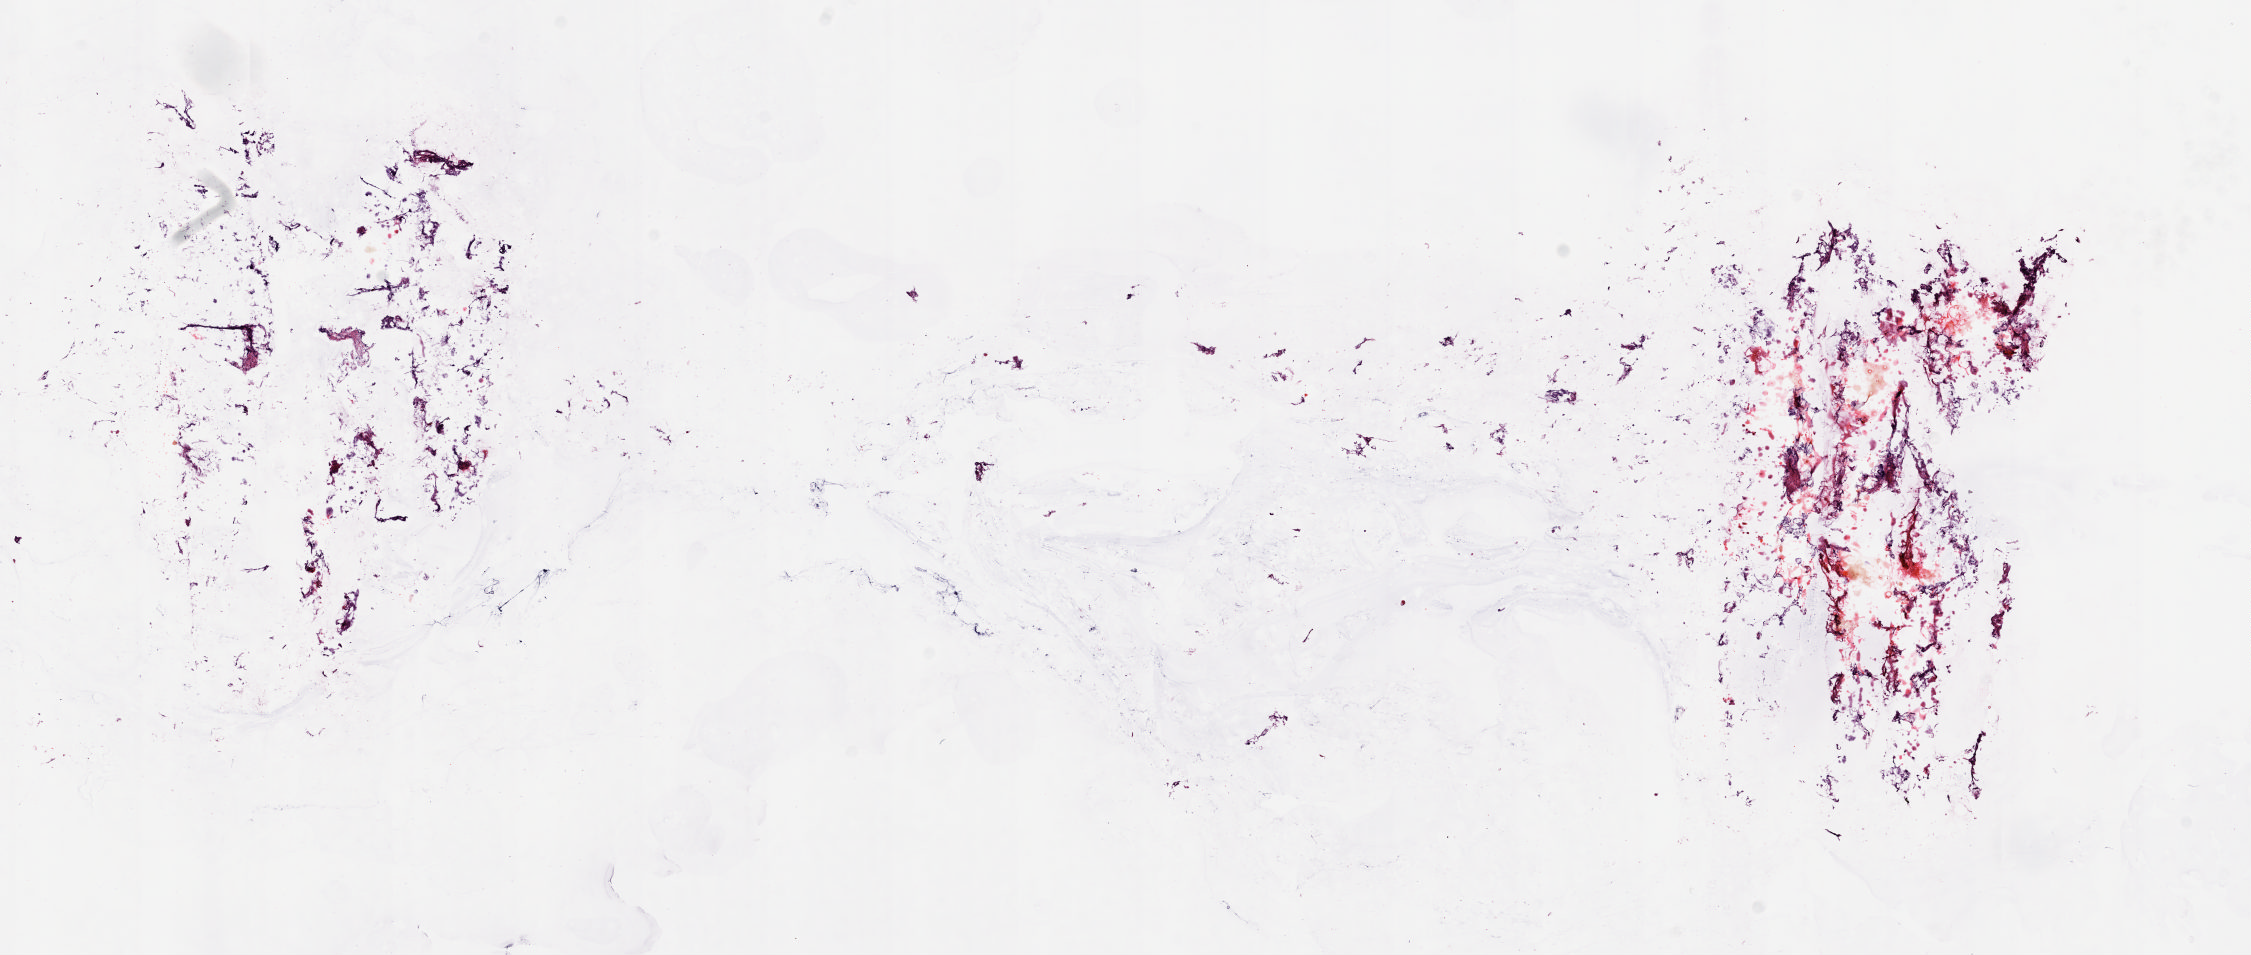
Whole-slide histology image, H&E-stained, a low-resolution overview of the entire scanned area, about 17.9 x 7.6 mm (acquisition: 20x scan); frozen section; sample: solid tissue normal (non-tumour tissue), thymus. Male patient; age at initial diagnosis 47 years. Composition of this section per pathologist review: tumour cells 0%, tumour nuclei 0%, normal cells 100%, stromal cells 0%, necrosis 0%. Inflammatory infiltration, as recorded: lymphocyte infiltration 0%, monocyte infiltration 0%, neutrophil infiltration 0%.
This section: solid tissue normal sample (biorepository sample class). Patient diagnosis: Thymoma, type B1, malignant.